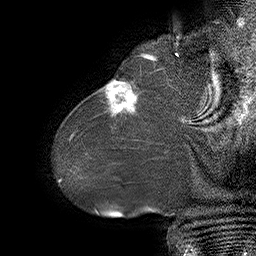
Breast MRI (dynamic contrast-enhanced), one sagittal slice. Position 9 of 55 along the scan axis. Dynamic contrast-enhanced series, time point 2 of 6 at this slice position (early post-contrast). 1.5 T. TE 4.5 ms, TR 32.4 ms. 3 mm slice thickness. 256 × 256 image matrix, field of view 180 × 180 mm. Female patient. From the clinical record (not read from this slice): setting: breast cancer imaged before/during neoadjuvant chemotherapy; receptor status: HER2-positive.
Annotated regions visible in this slice (semi-automatically segmented with operator editing):
- analysis volume of interest (the breast-tissue region the enhancement analysis was run in; not a lesion): bounding box (x1, y1, x2, y2) in pixels: (80, 64, 163, 134)
- tumour enhancement mask (voxels above the 100 % enhancement threshold inside the analysis volume of interest): (104, 79, 138, 116)